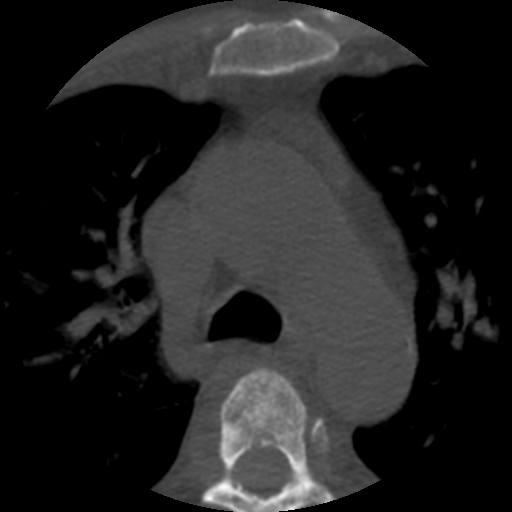
CT including the spine, one axial slice; position 395 of 508 along the scan axis; reconstruction kernel STANDARD; 120 kVp; bone window (W 1800 / L 400 HU); 1.25 mm slice thickness; 512 × 512 image matrix, field of view 160 × 160 mm. Patient age 57 years. Case-level facts recorded for this patient, not image findings: primary cancer: prostate.
Structures marked on this image (semi-automatically segmented with operator editing):
- T3 vertebra: bounding box [x1, y1, x2, y2] px = [235, 367, 295, 392]
- T4 vertebra: [202, 377, 331, 512]
- T5 vertebra: [218, 476, 244, 490]